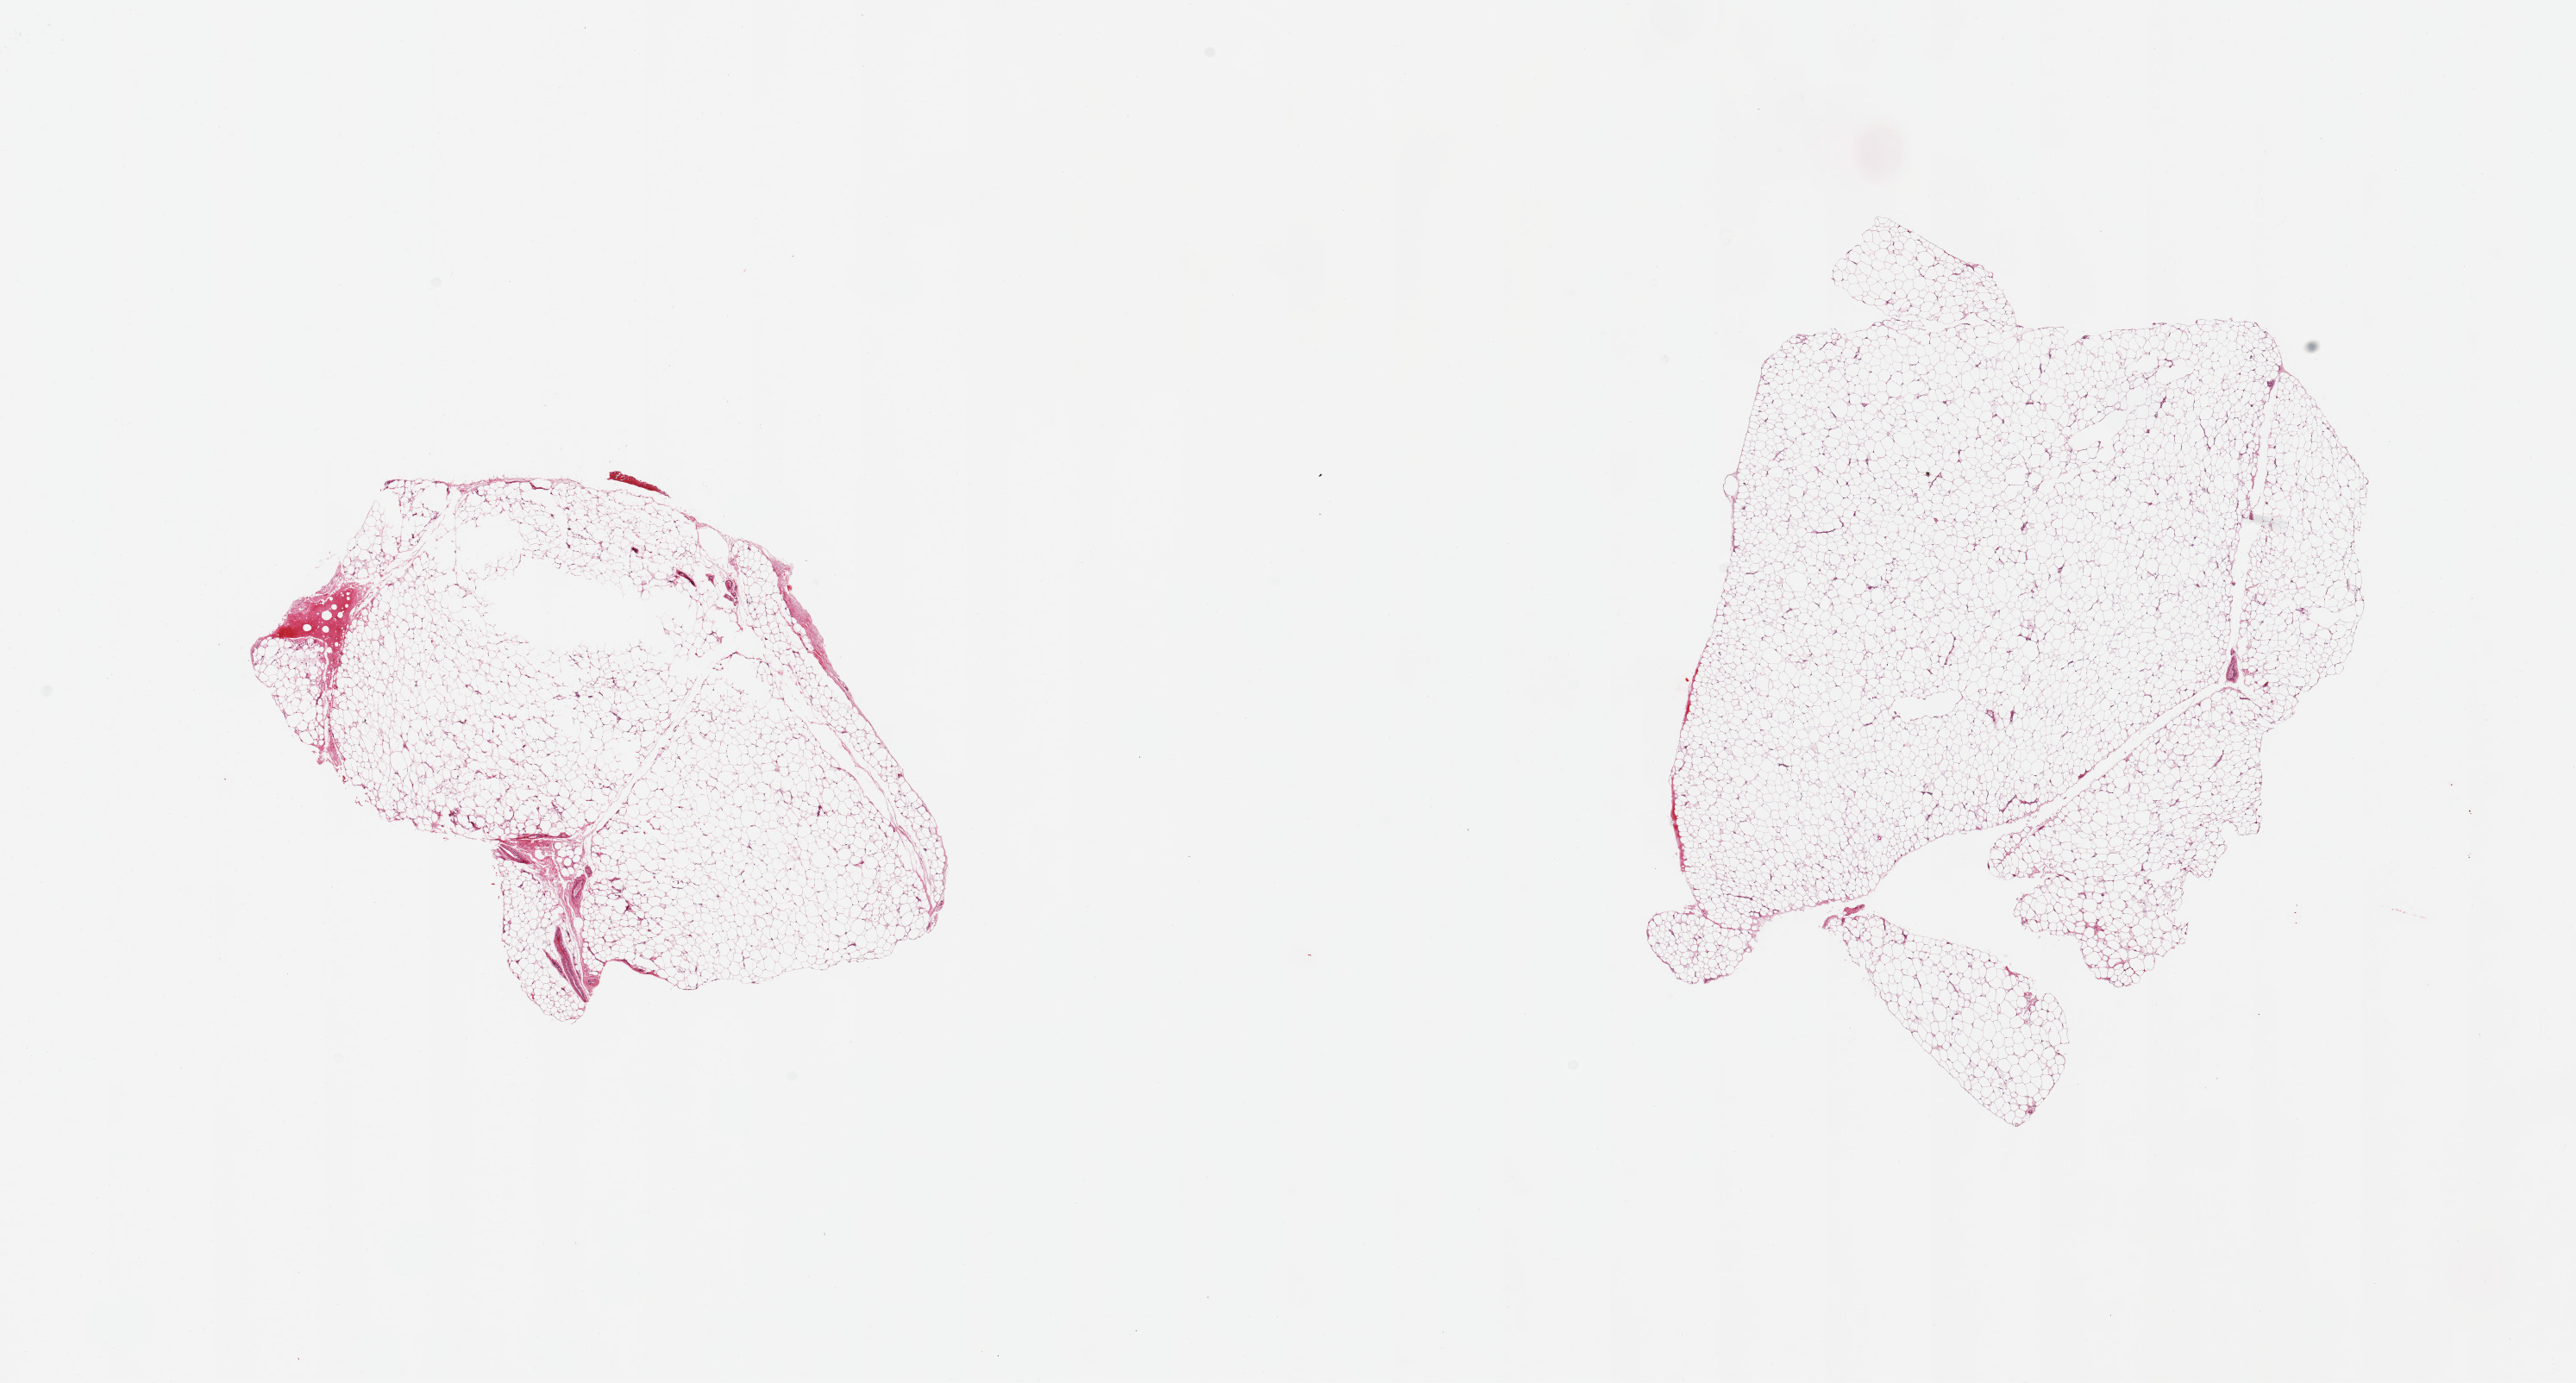
Whole-slide image, hematoxylin and eosin (H&E) stain, brightfield — whole scanned area (about 23.6 x 12.7 mm, slide scanned at 20x) shown as a low-resolution overview, PAXgene-fixed, paraffin-embedded tissue, sampled site (target tissue): adipose tissue, tissue donor sample. Donor: male.
Reviewer comment on this tissue sample: 2 pieces; low stromal content.